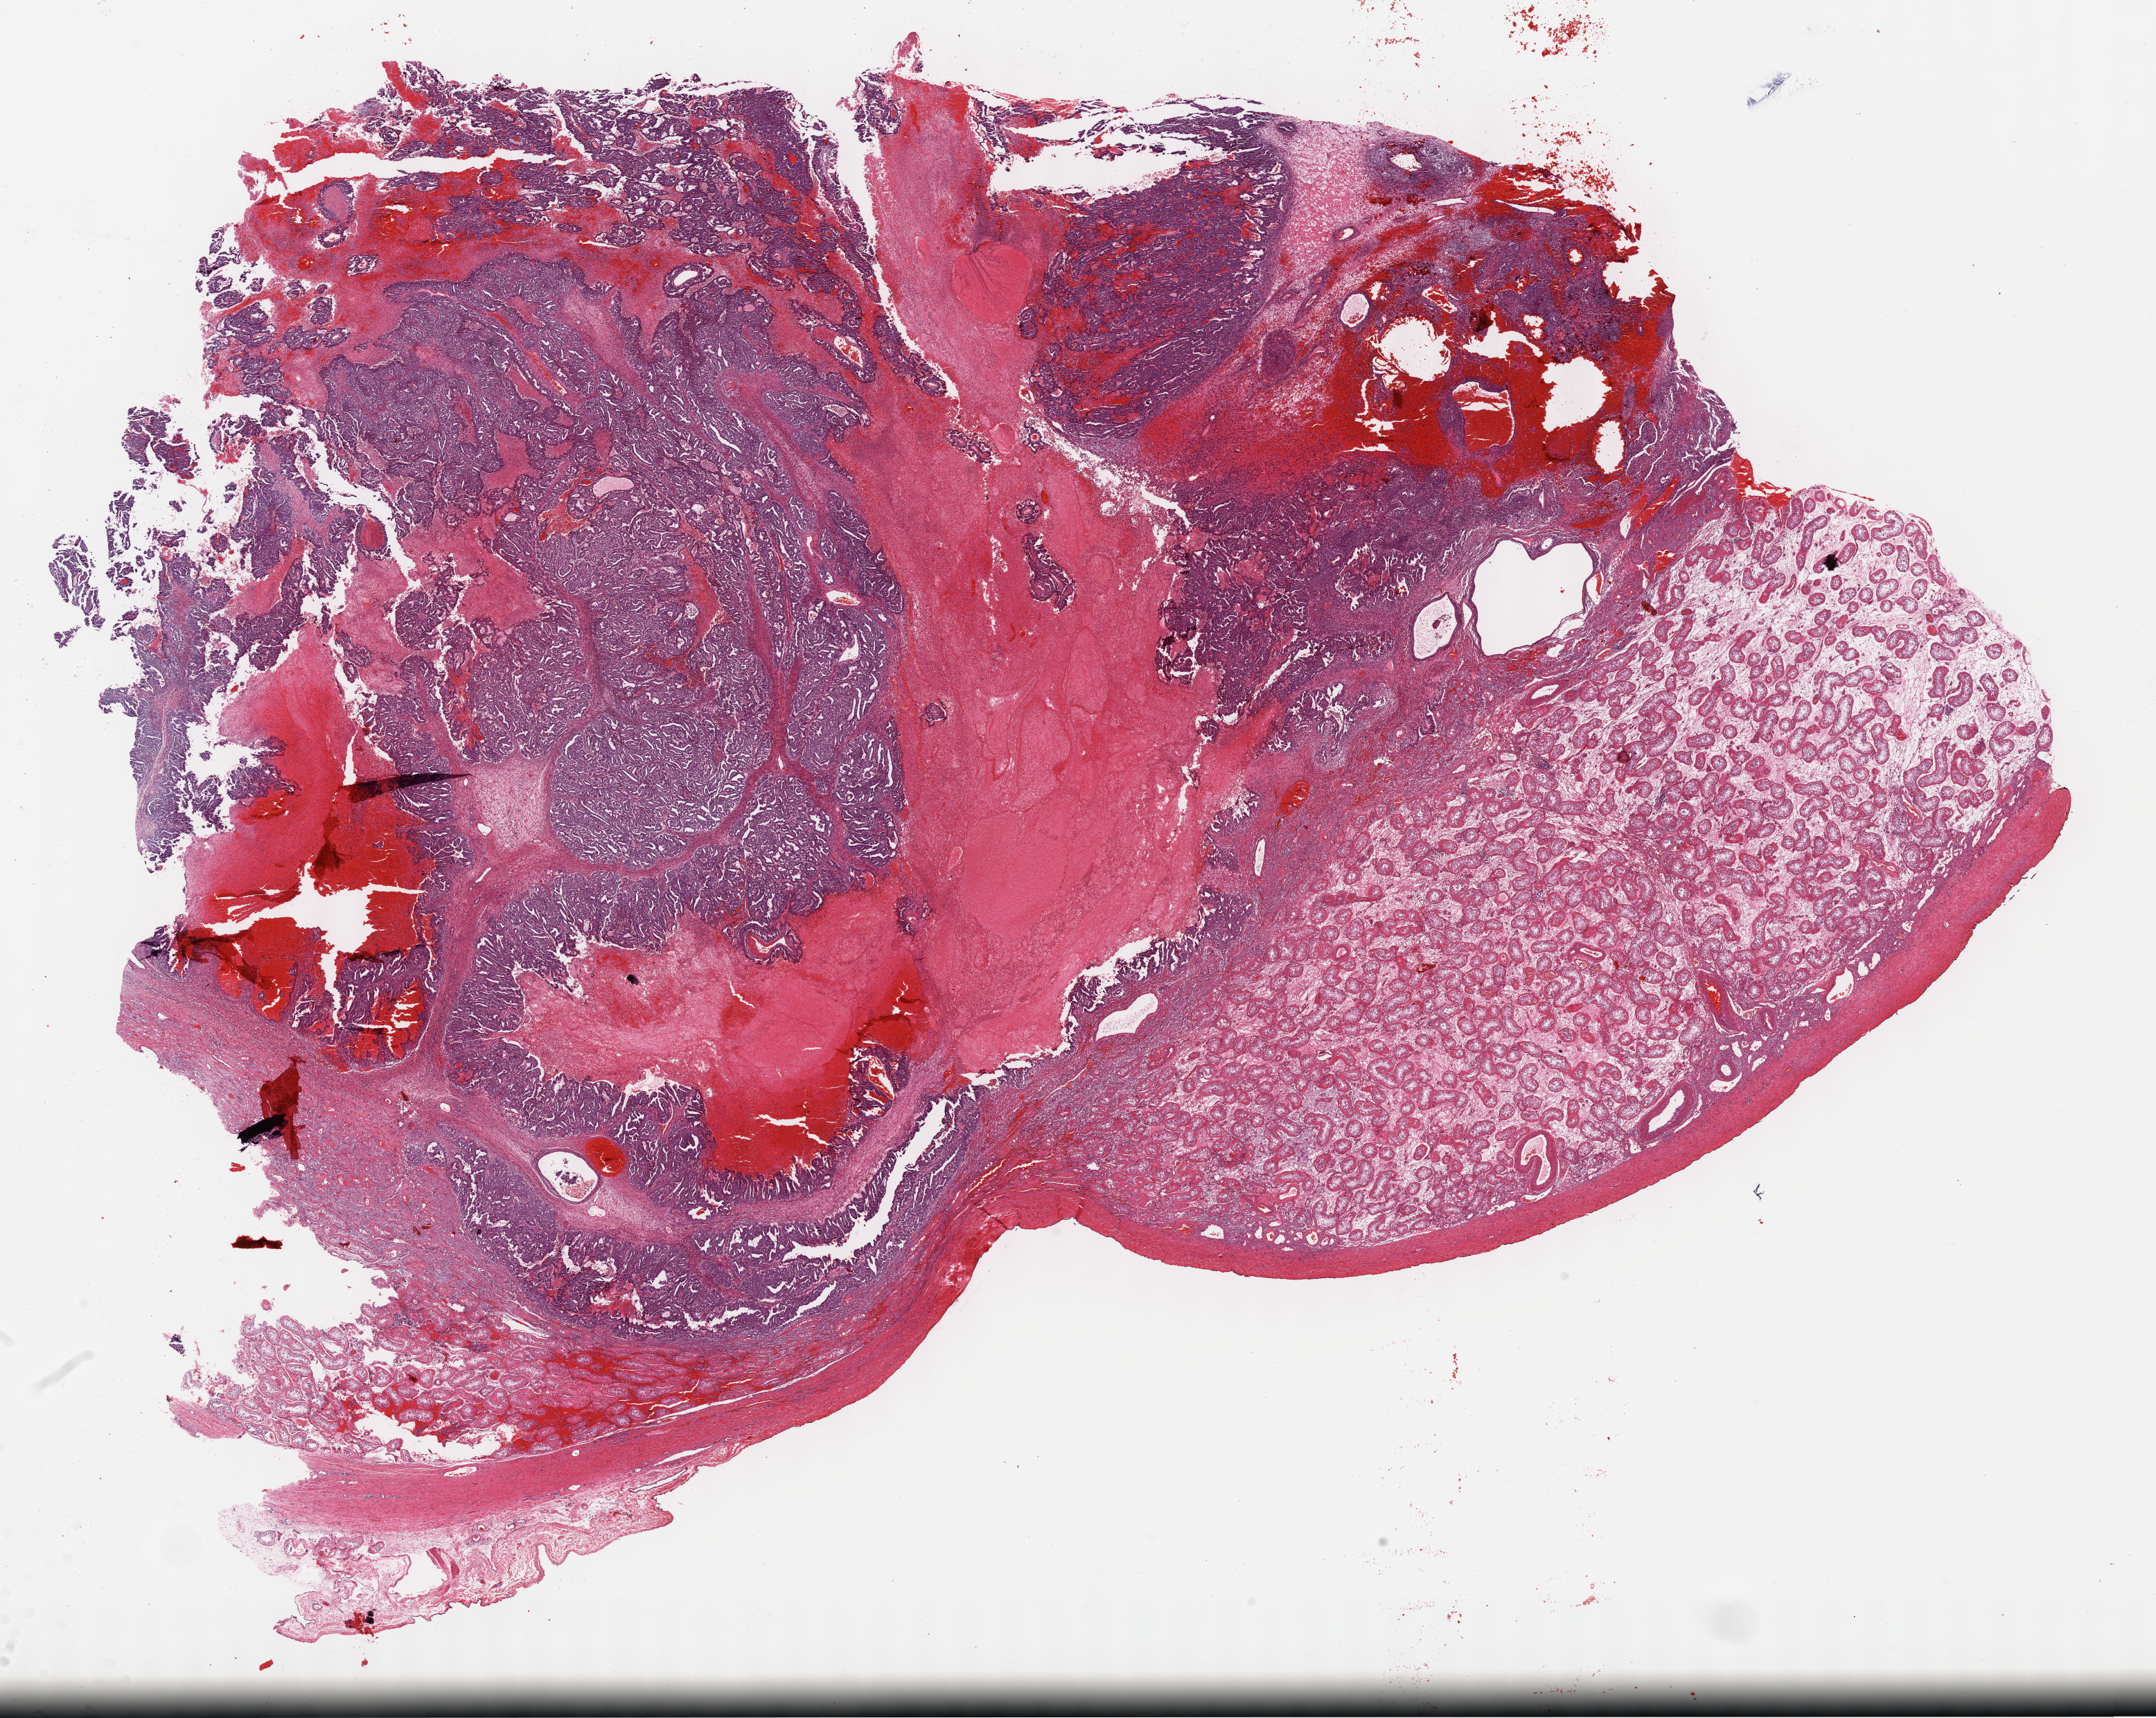
H&E whole-slide image — shown as a low-resolution overview of the whole scanned area (about 25.2 x 20.1 mm); formalin-fixed paraffin-embedded (FFPE) diagnostic section; sample: primary tumour, testis. Male patient; age at initial diagnosis 67 years.
Diagnosis: Embryonal carcinoma, NOS.